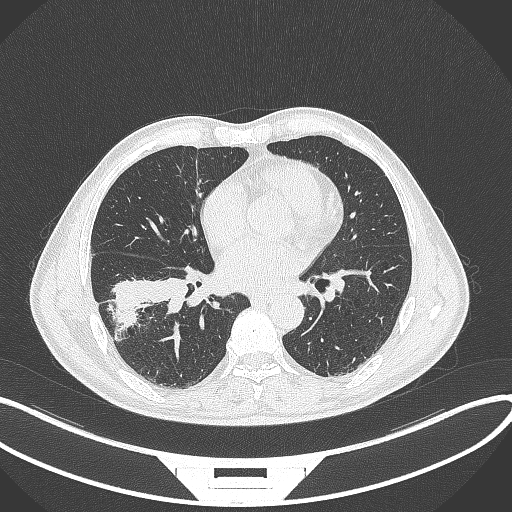
Chest CT, one axial slice. Position 162 of 364 along the scan axis. Reconstruction kernel B70f. 120 kVp. Lung window (W 1500 / L -600 HU). 1 mm slice thickness. 512 × 512 image matrix, field of view 400 × 400 mm. Male patient, age 58 years. From the clinical record (not read from this slice): clinical TNM (as recorded): T3 N0 M0.
Outlined on this slice (bounding box drawn by a radiologist):
- lung tumour (recorded histology: squamous cell carcinoma): bounding box <105,275,189,332> (left, top, right, bottom; pixels)